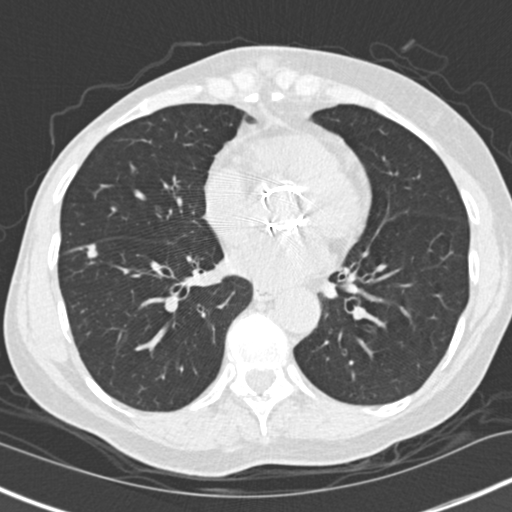
Low-dose screening chest CT, one axial slice. Lung window (W 1500 / L -600 HU). 2 mm slice thickness. 512 × 512 image matrix, field of view 307 × 307 mm.
Outlined on this slice (expert manual segmentation):
- lesion 1 (tumor, lower lobe of right lung): bounding box (x1, y1, x2, y2) in pixels: (87, 244, 97, 258)